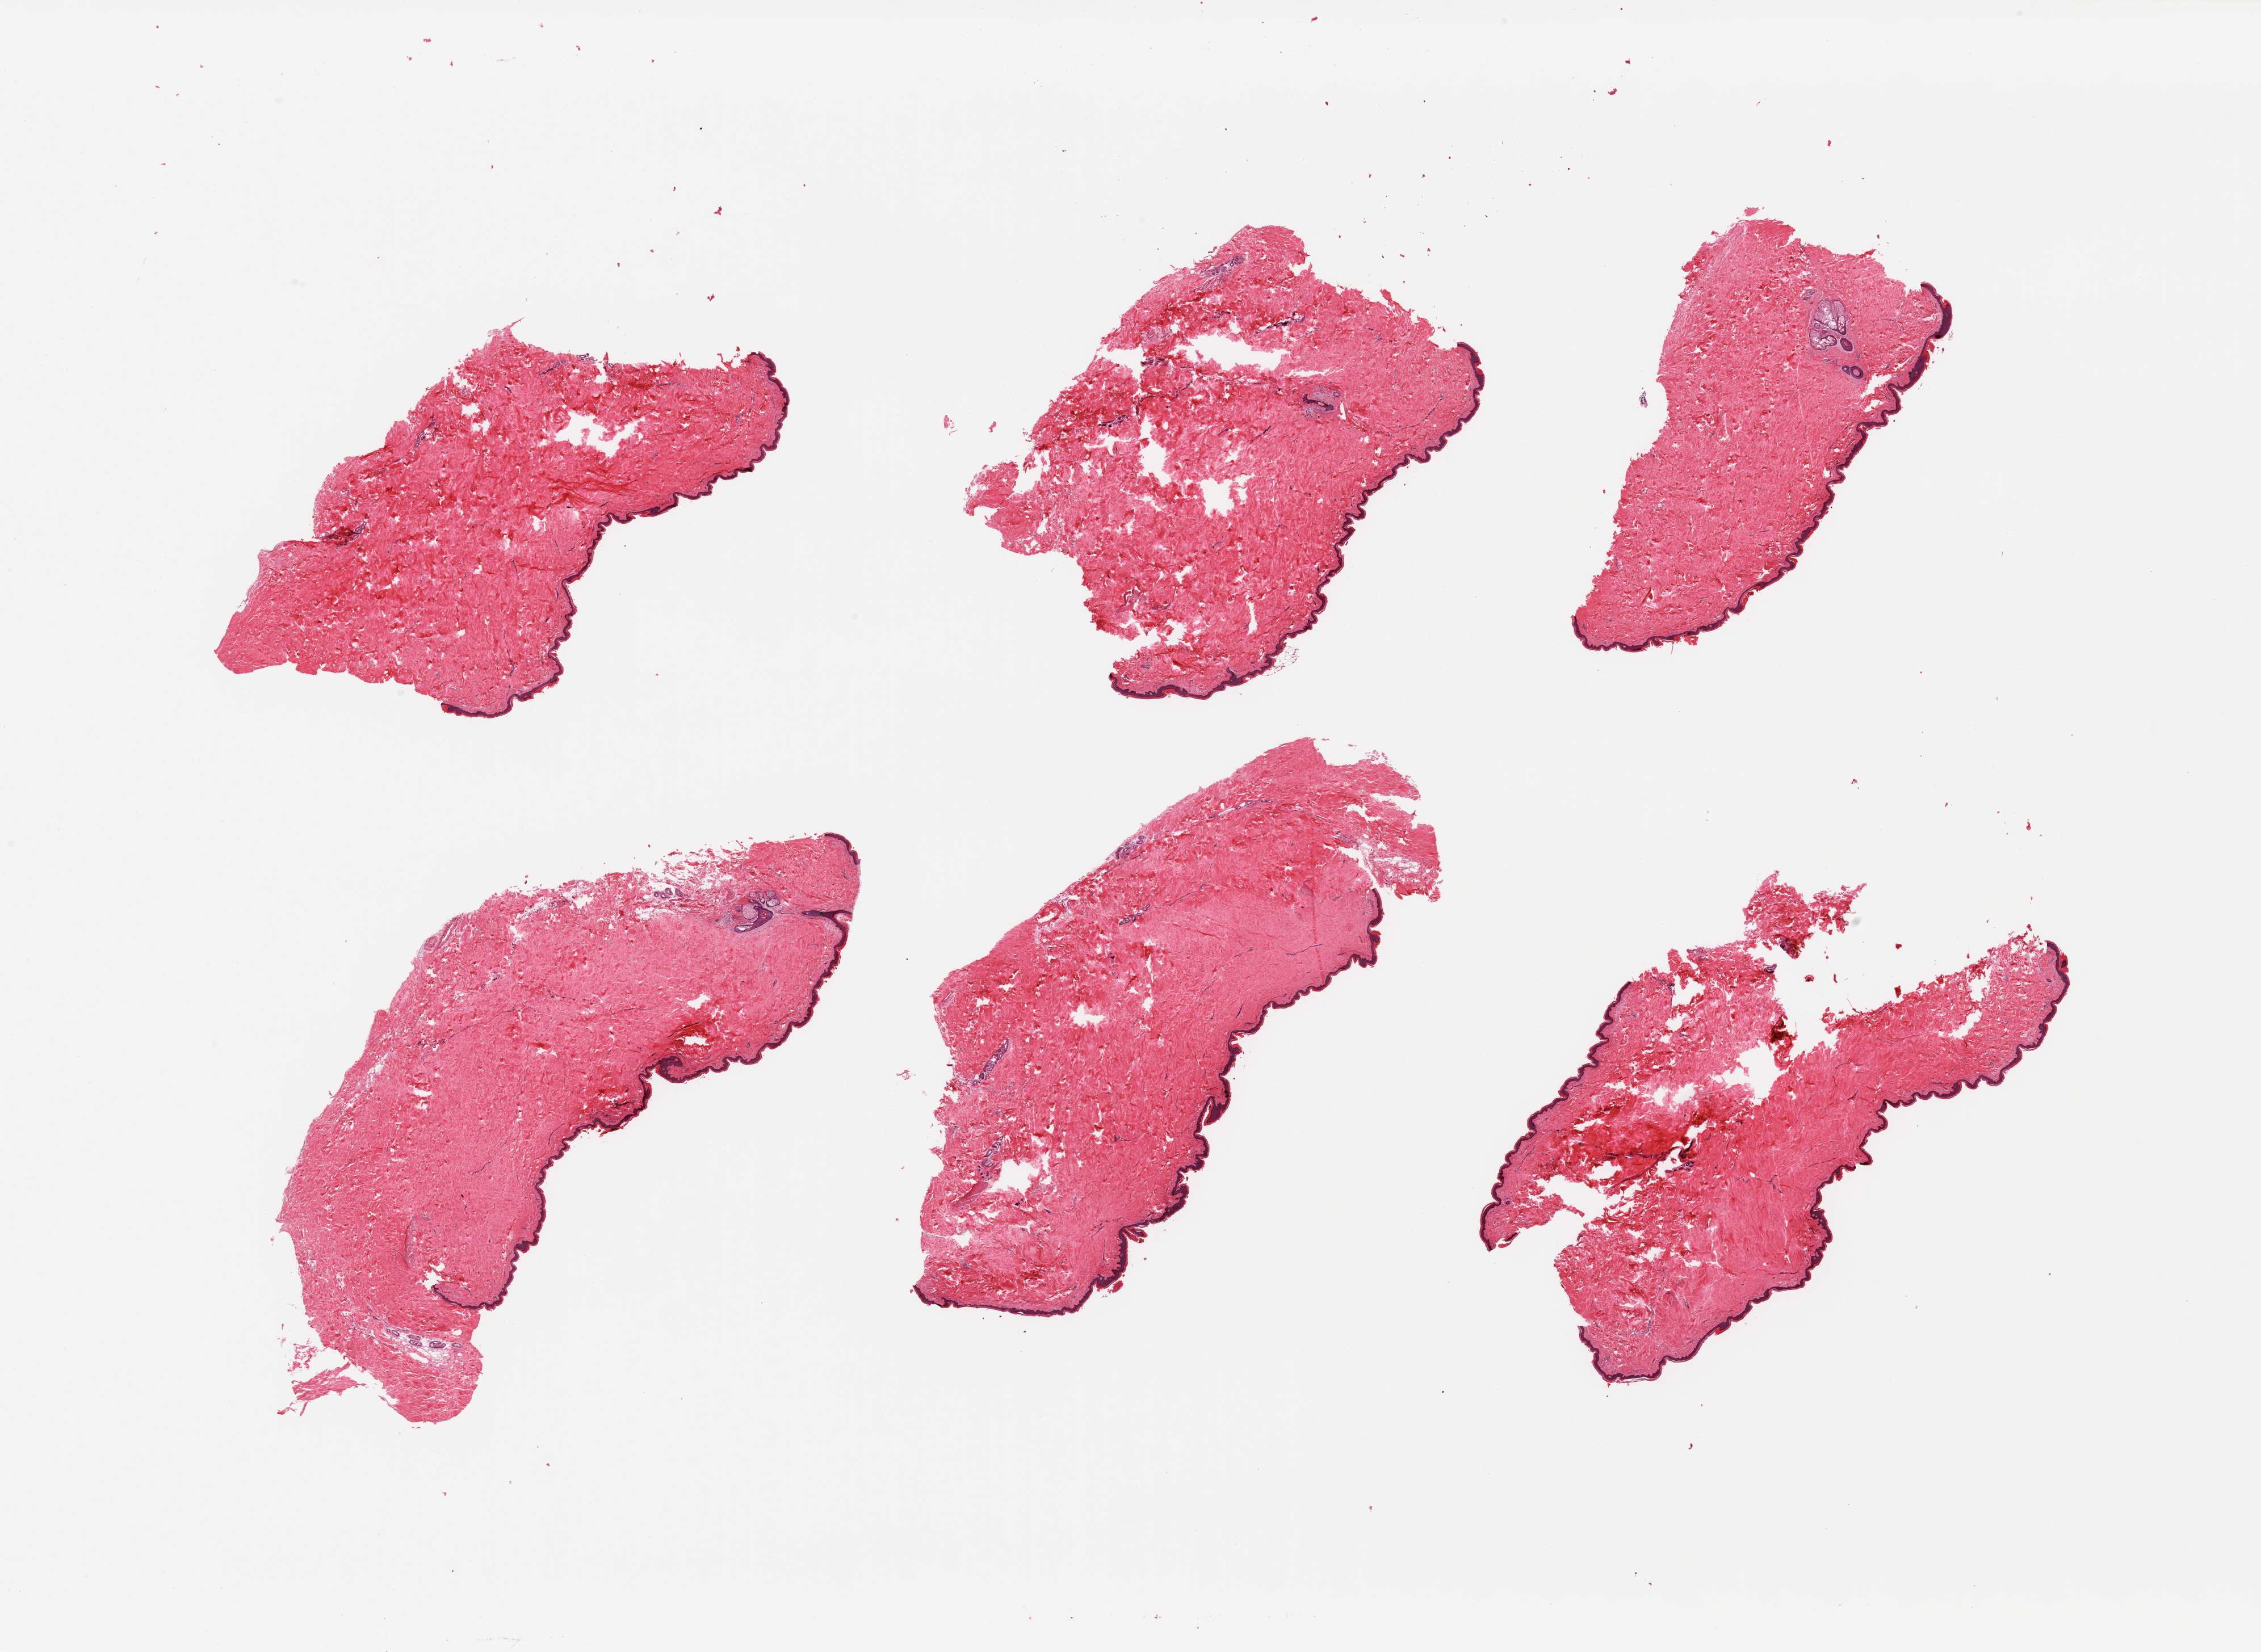
Whole-slide image, haematoxylin and eosin stain, brightfield — shown as a low-resolution overview of the whole scanned area (about 31.5 x 23.0 mm, acquisition: 20x scan). PAXgene-fixed, paraffin-embedded tissue. Section of skin of suprapubic region (target tissue). Donor tissue sample.
* pathologist's review note for this sample: 6 pieces; well trimmed